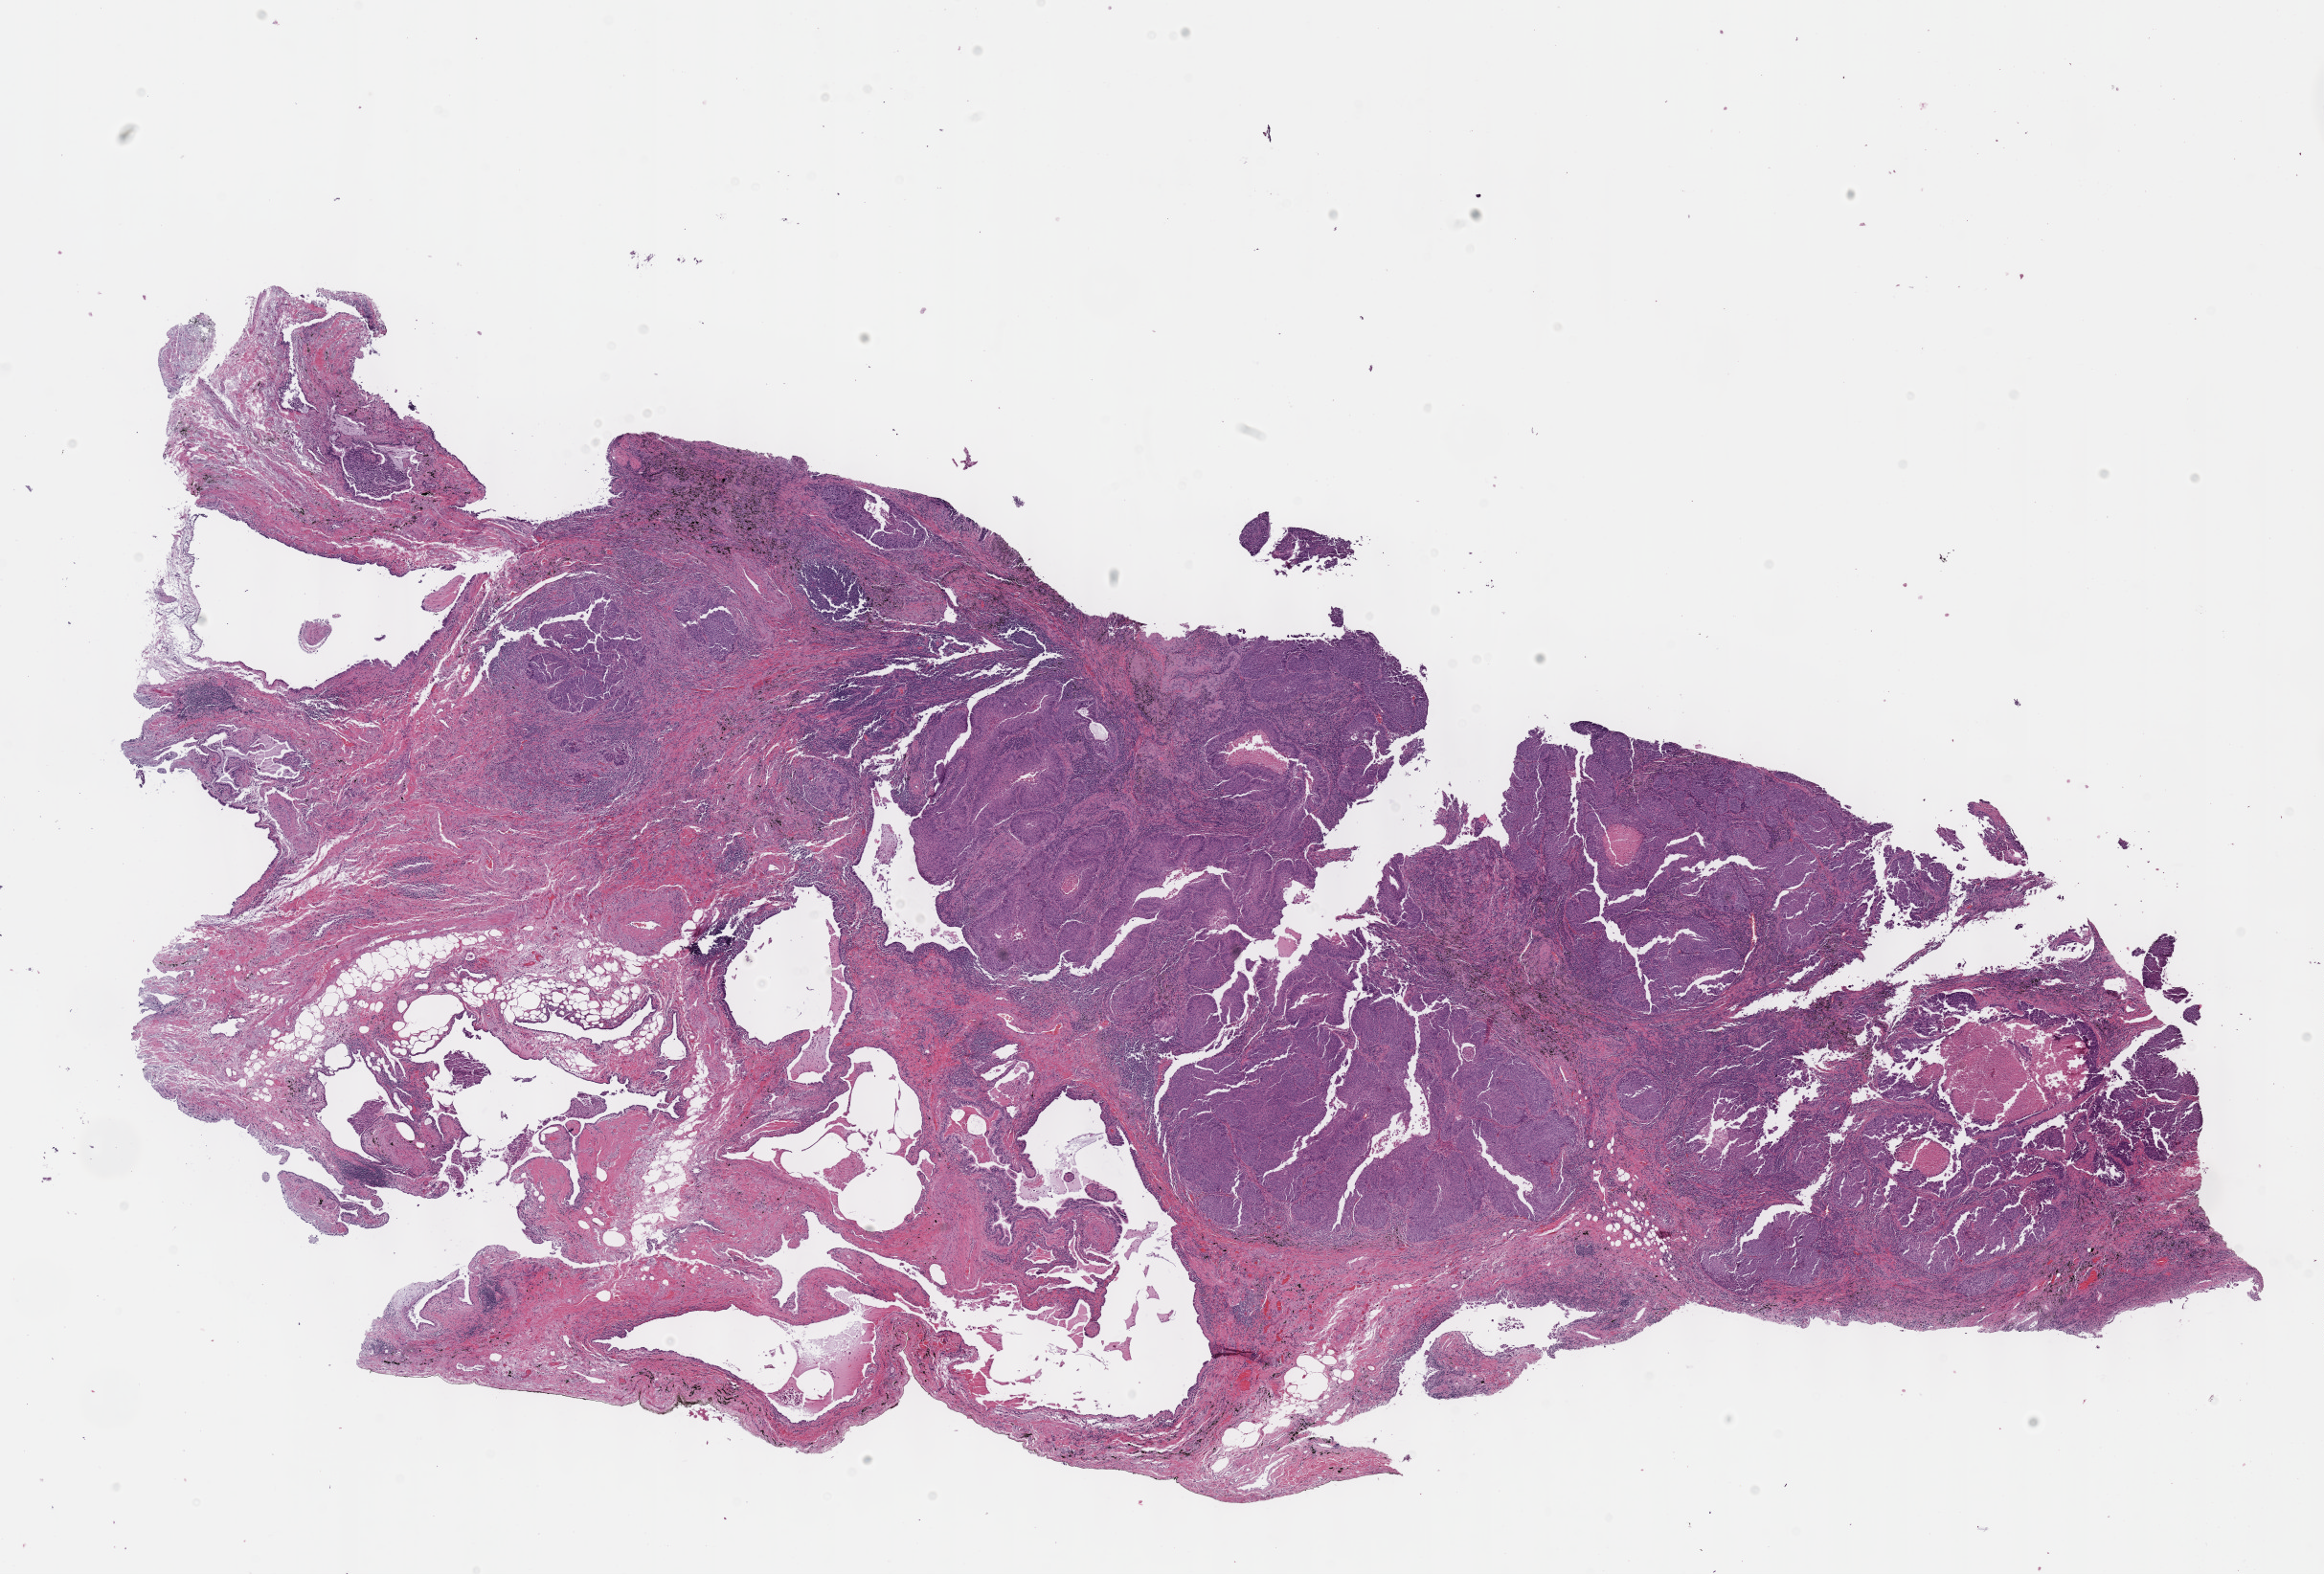
H&E-stained whole-slide image — whole scanned area (about 19.6 x 13.3 mm, acquisition: 40x scan) shown as a low-resolution overview; FFPE section; primary tumour sample from the lung. Male, age 74 years at initial diagnosis.
Histologic diagnosis: Squamous cell carcinoma, NOS (upper lobe, lung). TNM: T2a N0 M0. AJCC pathologic stage: IB.